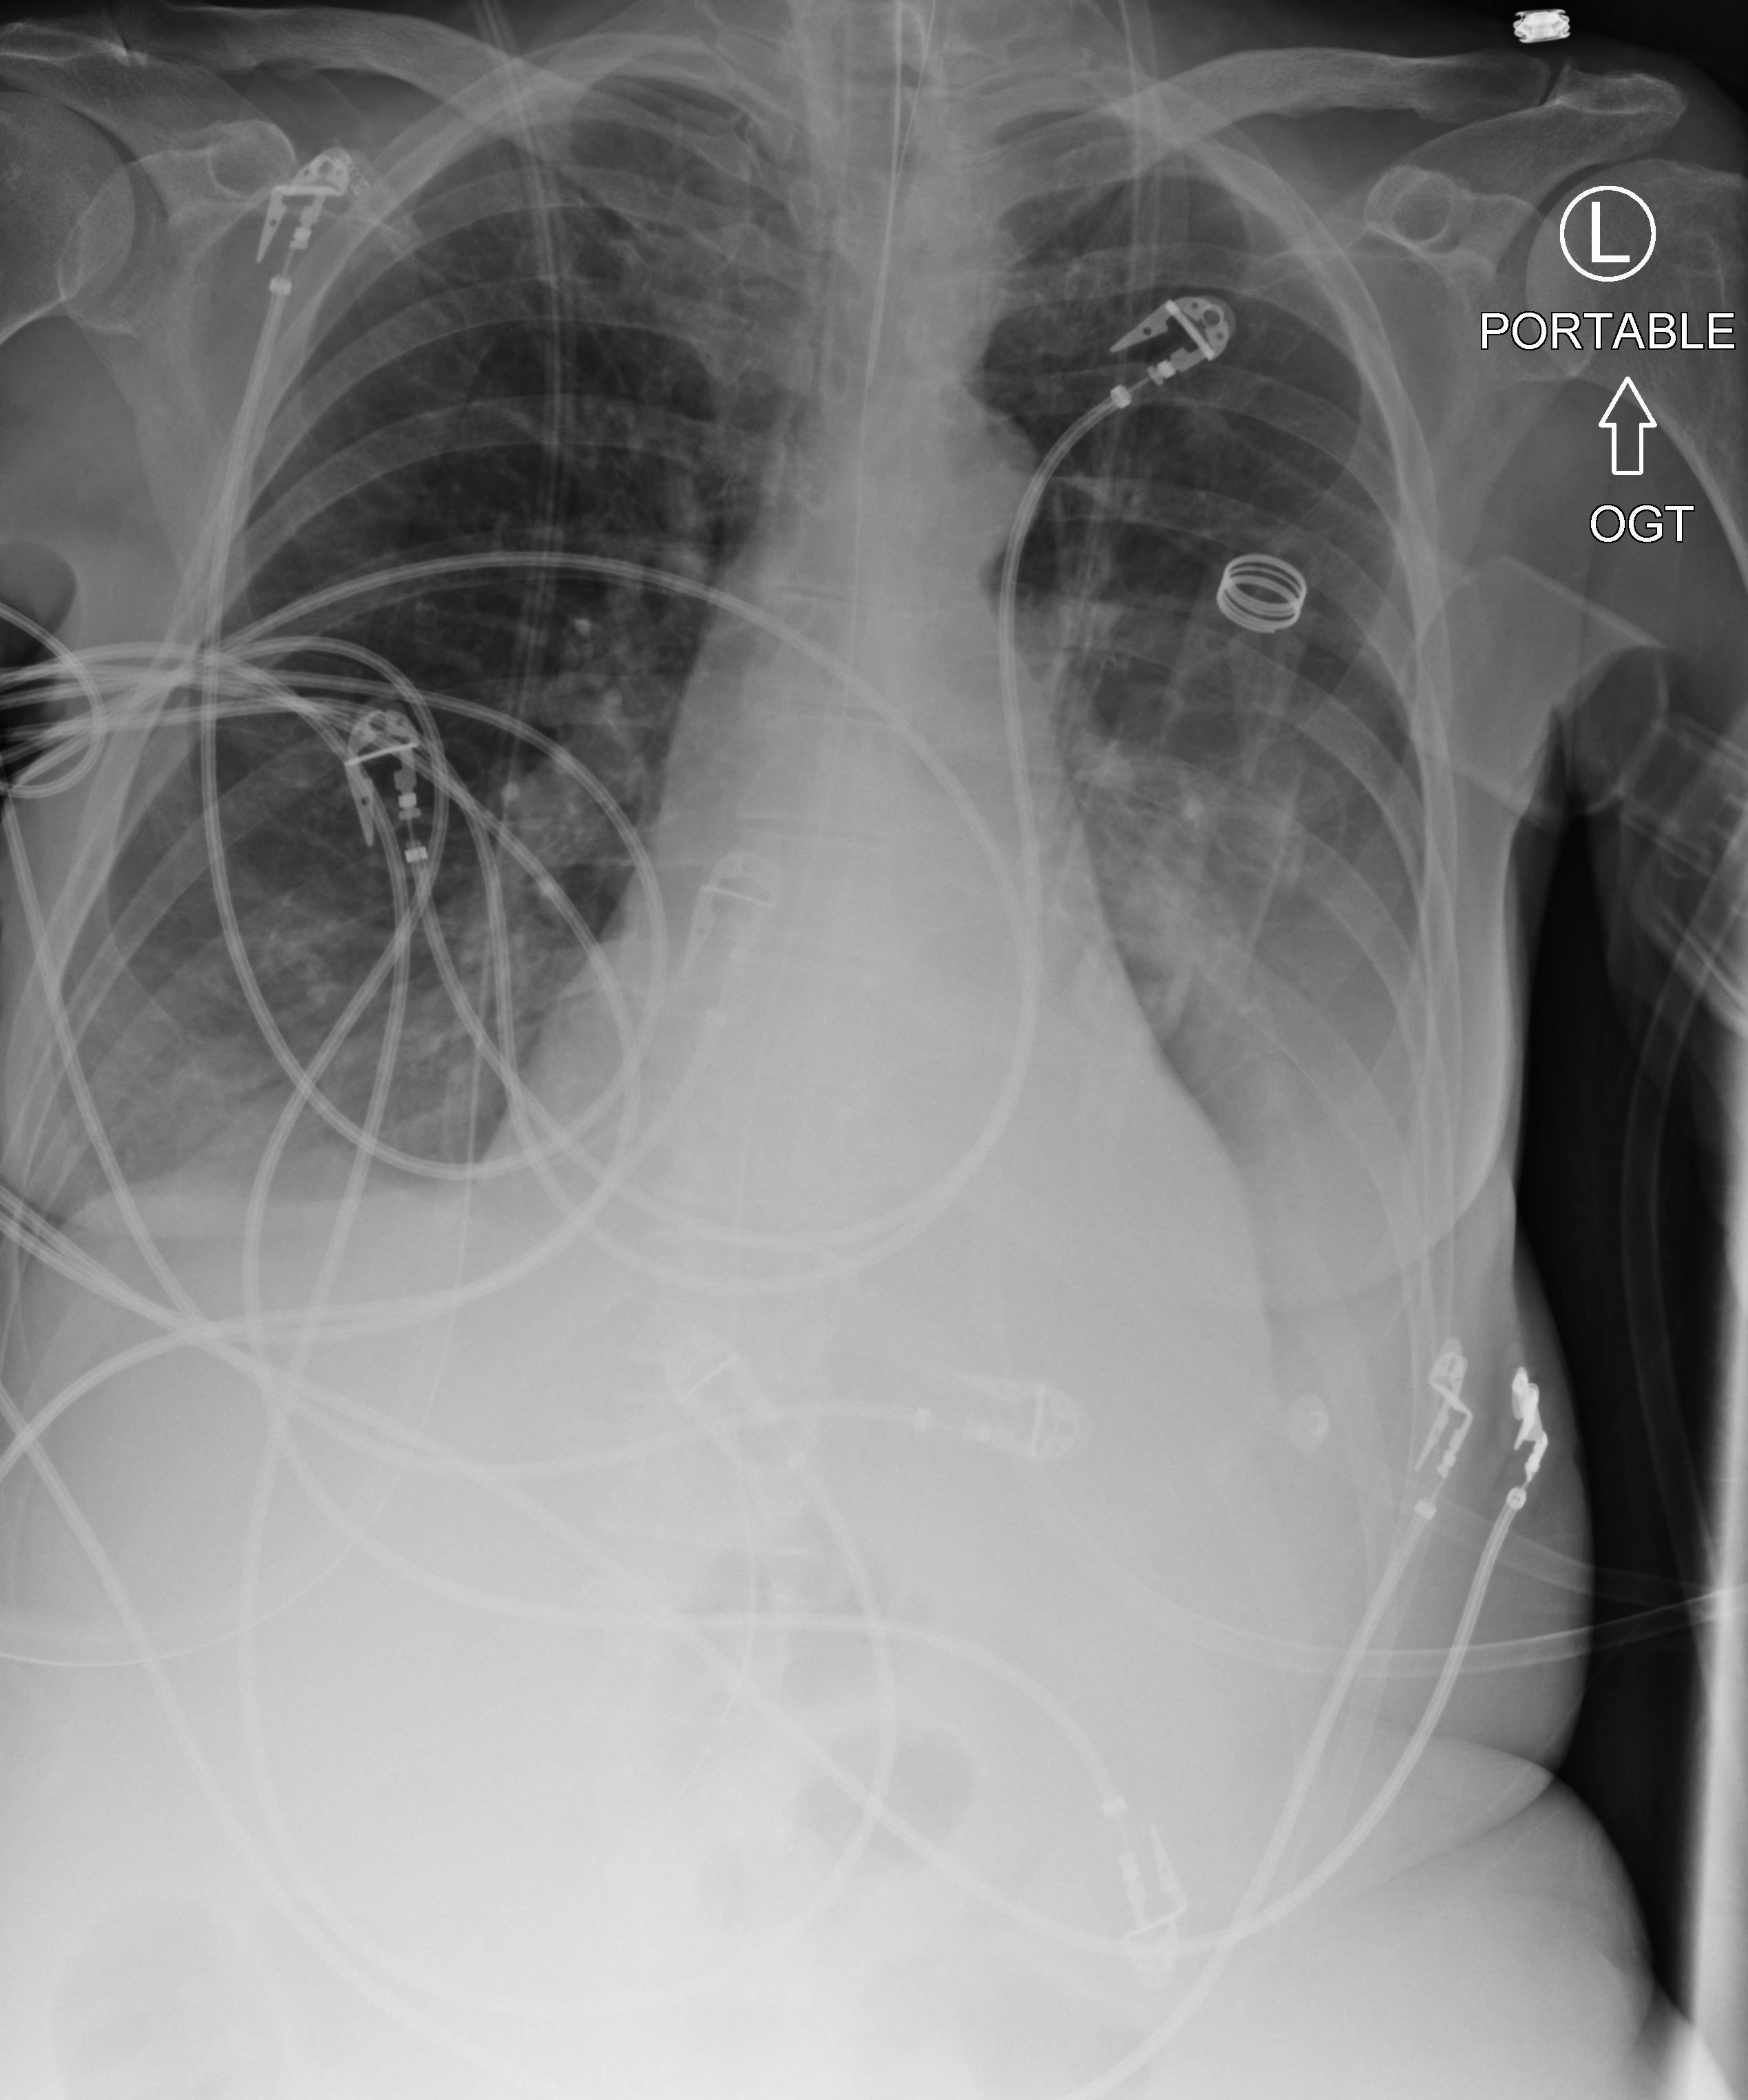
Chest X-ray (portable); anteroposterior (AP) projection. Female patient hospitalised with COVID-19, age 60–74 years.
Hospital-stay facts (about this admission, not read from this image; timing relative to this image not recorded): admitted to intensive care during this hospital stay: yes.